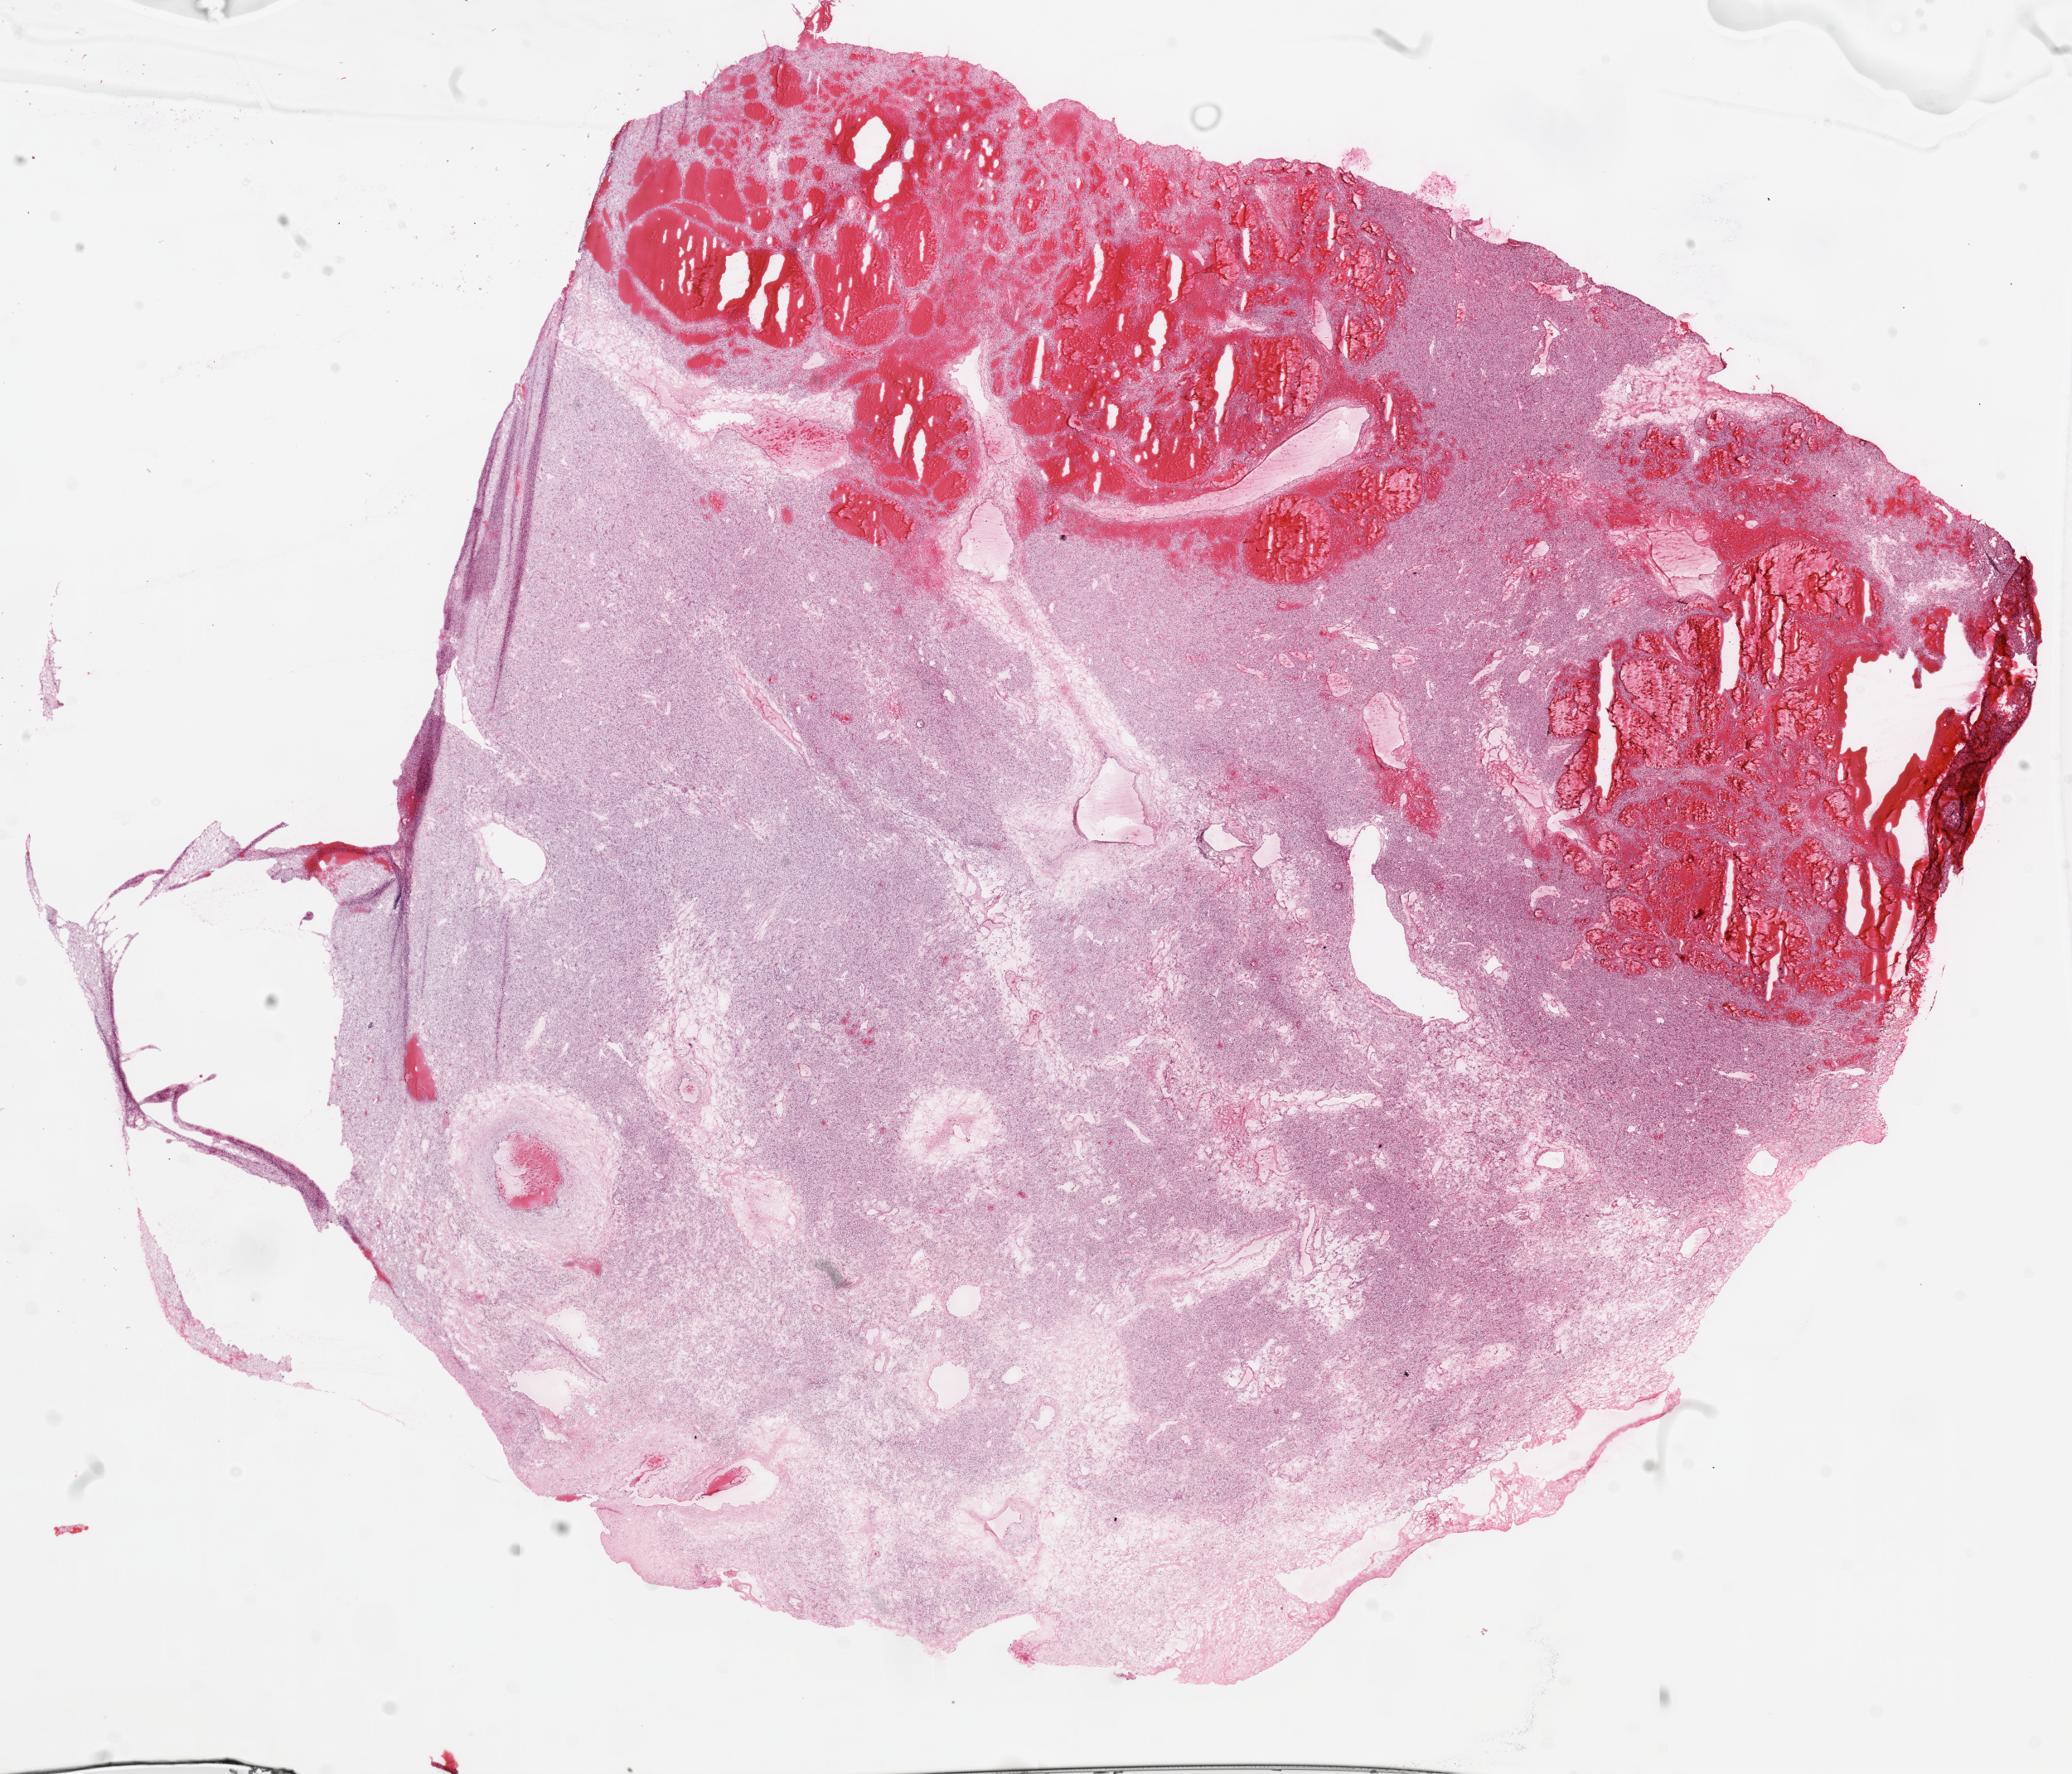
Digitized Hematoxylin and eosin (H&E) stained tissue section (whole slide), shown as a low-resolution overview of the whole scanned area (about 20.1 x 17.2 mm, acquisition: 20x scan), frozen section, primary tumour sample from the kidney. Female patient; age at initial diagnosis 86 years.
Histologic diagnosis: Clear cell adenocarcinoma, NOS.